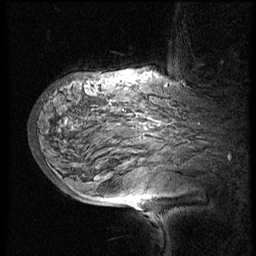
Breast MRI (dynamic contrast-enhanced), one sagittal slice; position 44 of 60 along the scan axis; 3 images stored at this slice position (order not interpretable as contrast timing); 1.5 T; TE 4.2 ms, TR 8.9 ms; 2.5 mm slice thickness; 256 × 256 image matrix, field of view 200 × 200 mm. Patient: female, 57 years. From the clinical record (not read from this slice): setting: breast cancer imaged before/during neoadjuvant chemotherapy; receptor status: HER2-positive.
Structures marked on this image (semi-automatically segmented with operator editing):
- analysis volume of interest (the breast-tissue region the enhancement analysis was run in; not a lesion): box from (x=34, y=75) to (x=214, y=171) px
- tumour enhancement mask (voxels above the 140 % enhancement threshold inside the analysis volume of interest): (x=66, y=122)–(x=68, y=124)